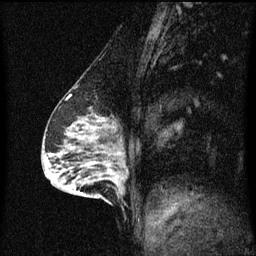
Breast MRI (dynamic contrast-enhanced), one sagittal slice; slice 25 of 60 in the series (ordered by position); dynamic contrast-enhanced series, image 2 of 3 at this slice position (ordered by acquisition); 1.5 T; TE 4.2 ms, TR 8.4 ms; 2 mm slice thickness; 256 × 256 image matrix, field of view 200 × 200 mm. Patient: female, 64 years.
Annotated regions visible in this slice (semi-automatically segmented with operator editing):
- analysis volume of interest (the breast-tissue region the enhancement analysis was run in; not a lesion): bounding box [x1, y1, x2, y2] px = [90, 164, 129, 203]
- tumour enhancement mask (voxels above the 70 % enhancement threshold inside the analysis volume of interest): [122, 170, 129, 193]